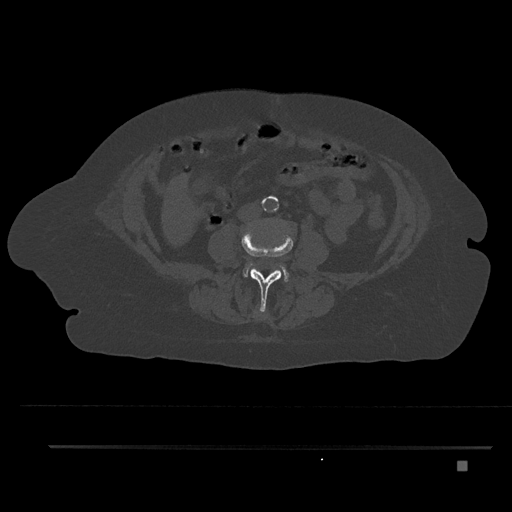
CT including the spine, one axial slice; slice 115 of 797 in the series (ordered by position); 120 kVp; bone window (W 1800 / L 400 HU); 512 × 512 image matrix. Female patient, age 76 years. From the clinical record (not read from this slice): primary cancer: lung; vertebrae with lytic lesions (as recorded): T11, L3.
Annotated regions visible in this slice (semi-automatic segmentation, software-assisted and operator-edited):
- L2 vertebra: bounding box <255,311,263,315> (left, top, right, bottom; pixels)
- L3 vertebra: <241,228,293,311>
- L4 vertebra: <244,262,289,282>